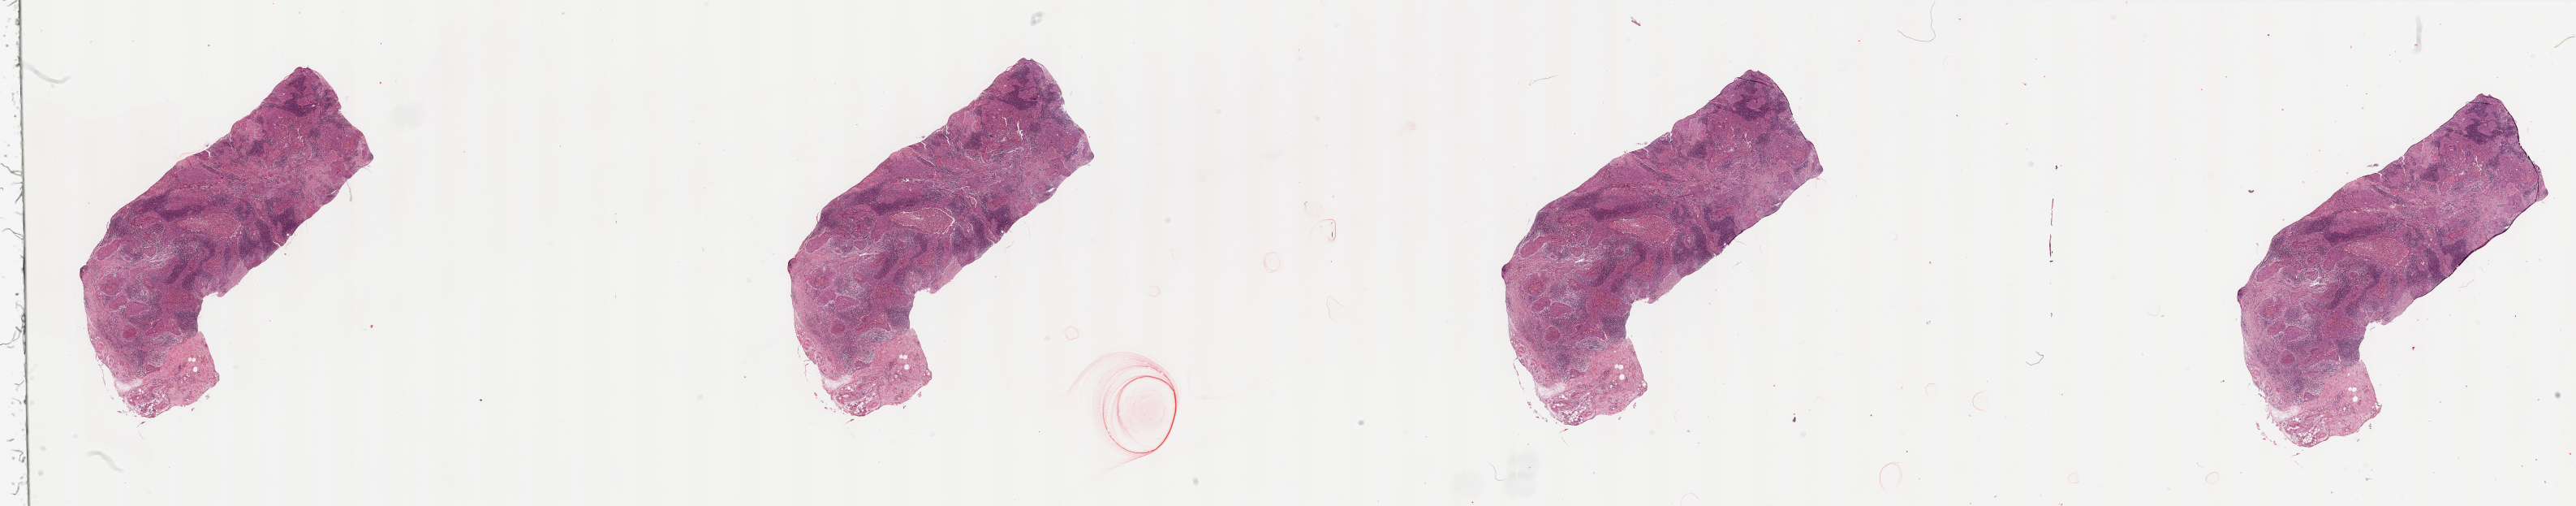
H&E-stained whole-slide image — low-resolution overview of the scanned area, about 50.2 x 9.9 mm. Head and neck, tissue type not recorded. 68-year-old male patient.
* patient diagnosis: Squamous cell carcinoma, NOS (larynx, NOS)